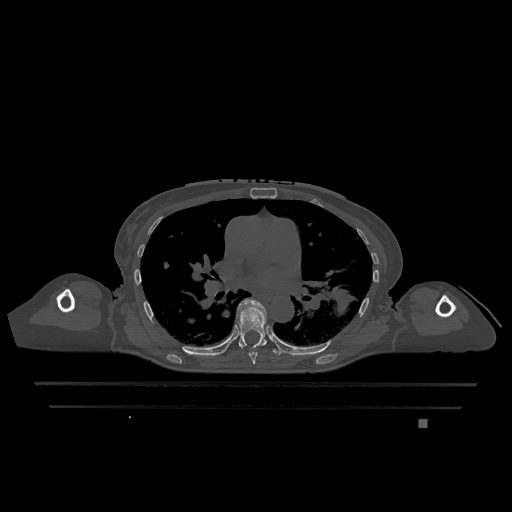
CT including the spine, one axial slice; bone window (W 1800 / L 400 HU); 0.5 mm slice thickness; 512 × 512 image matrix. Female patient, age 74 years. Case-level facts recorded for this patient, not image findings: primary cancer: lung; vertebrae with lytic lesions (as recorded): T1, T4, T5, T6, L4, L5.
Annotated regions visible in this slice (semi-automatically segmented with operator editing):
- T6 vertebra: bounding box (x1, y1, x2, y2) in pixels: (241, 346, 258, 364)
- T7 vertebra: (237, 299, 281, 355)